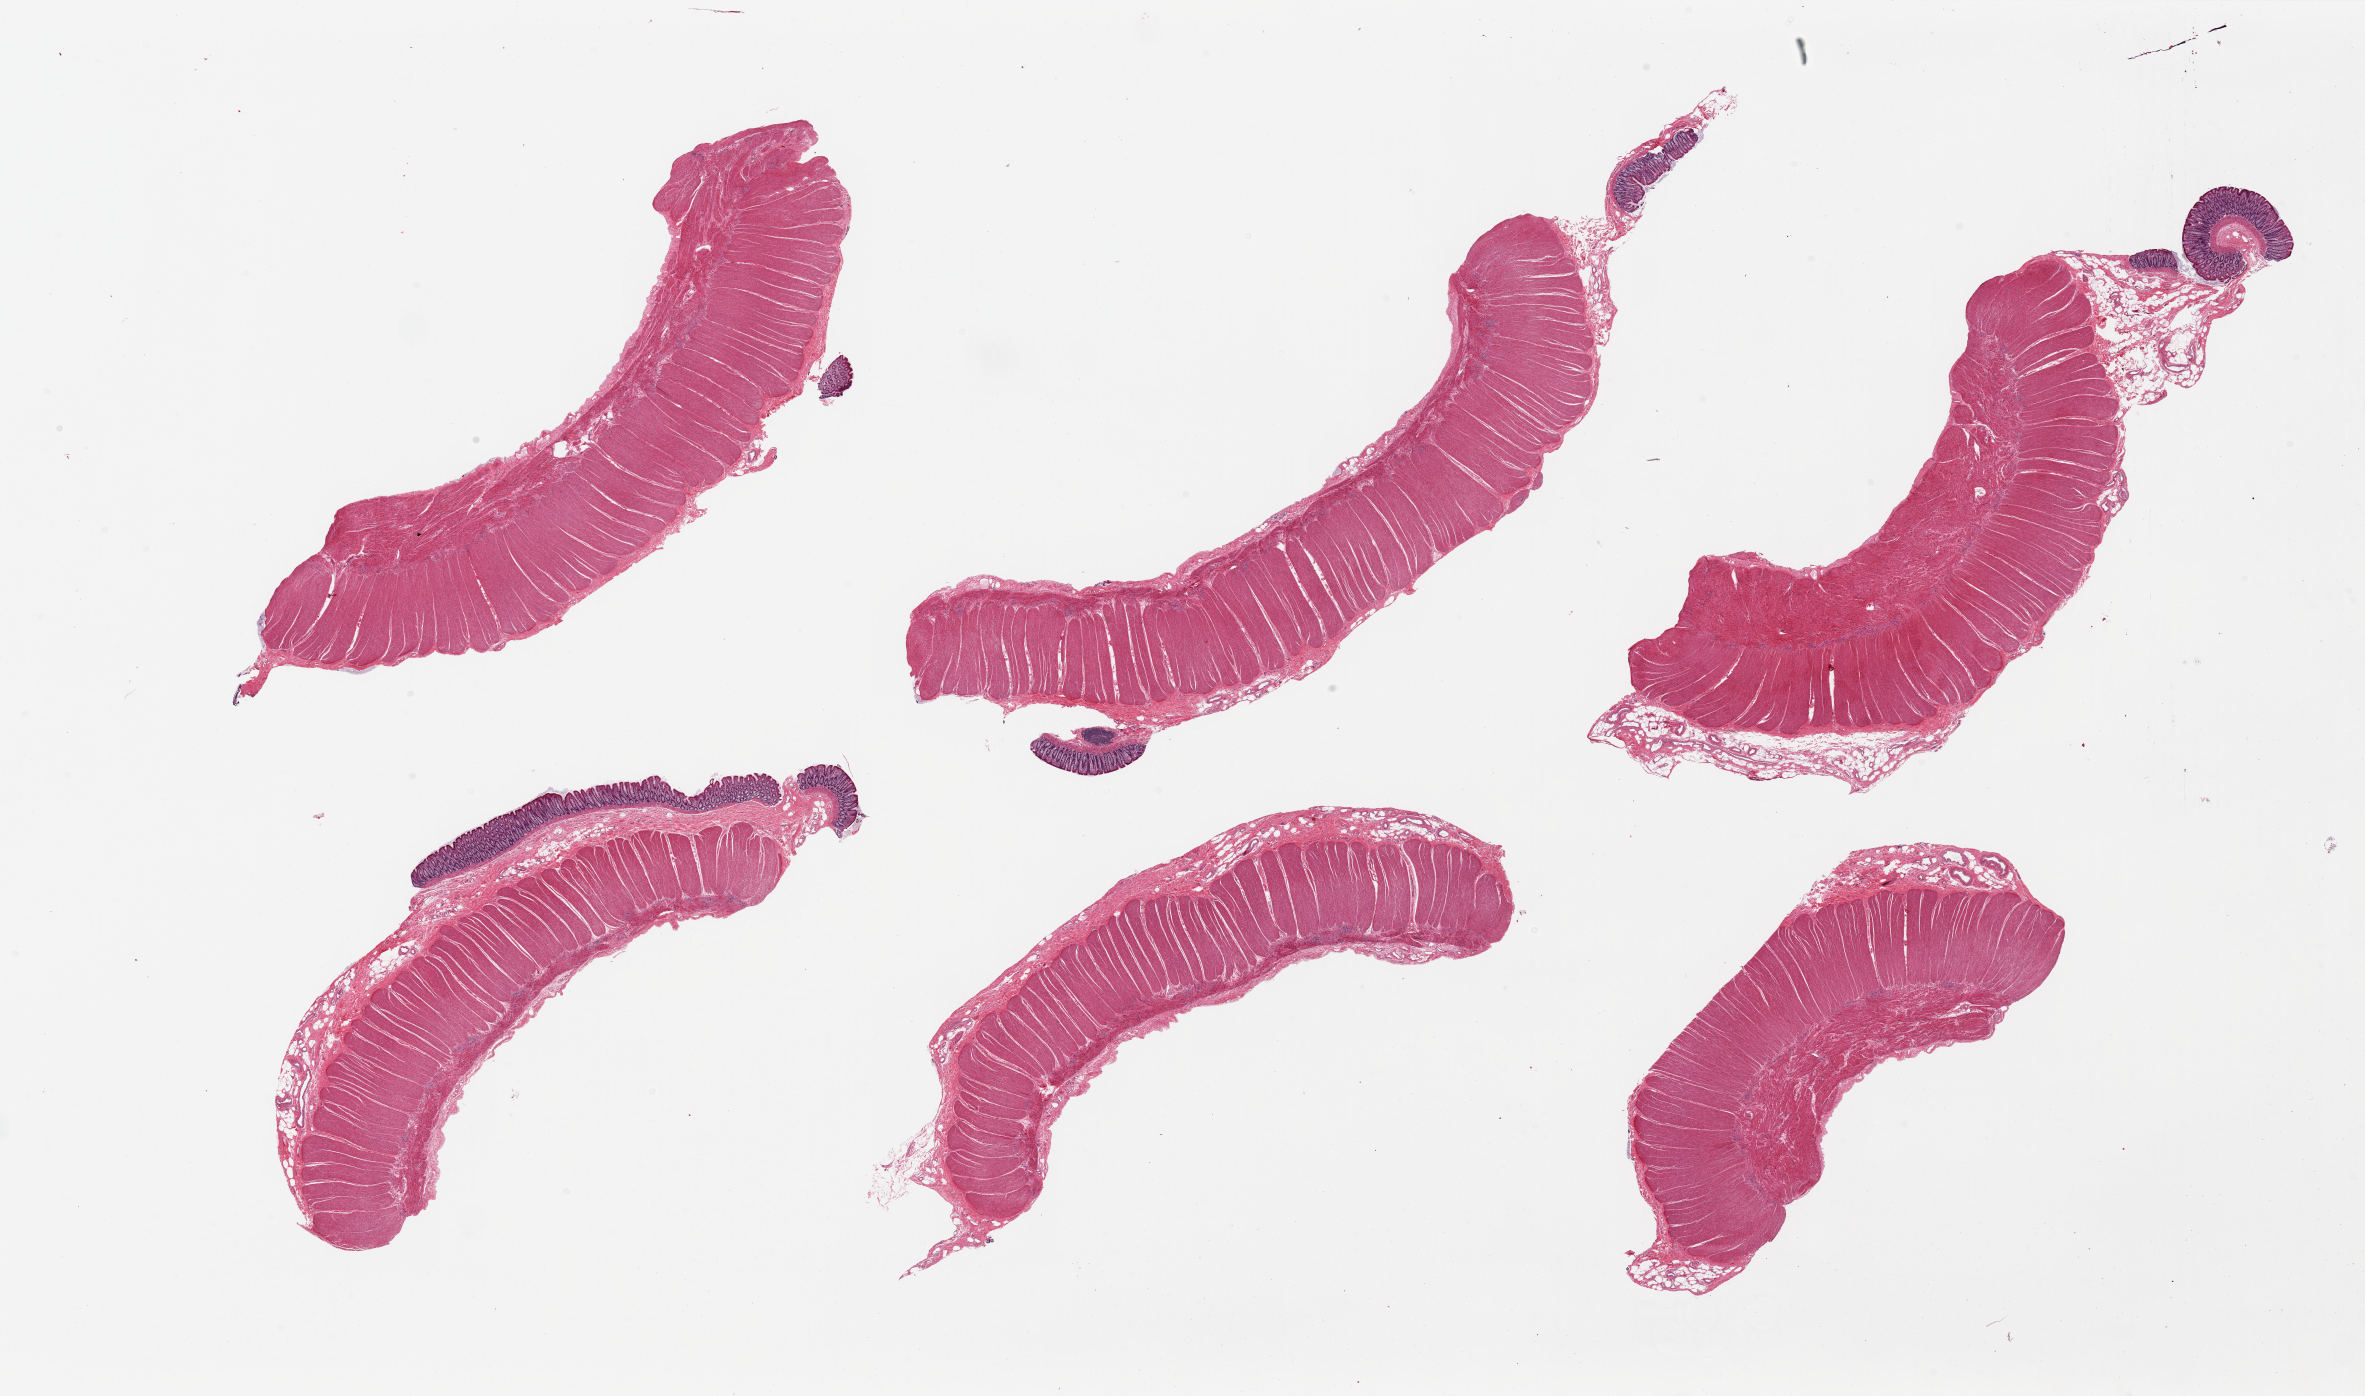
Whole-slide image, H&E stain — whole scanned area (about 37.4 x 22.1 mm, acquisition: 20x scan) shown as a low-resolution overview. PAXgene-fixed, paraffin-embedded tissue. Sampled site (target tissue): sigmoid colon. Donor tissue sample. Donor: female.
• pathologist's review note for this sample: 6 pieces; 4 pieces have mucosa (not target) up to 7mm in length